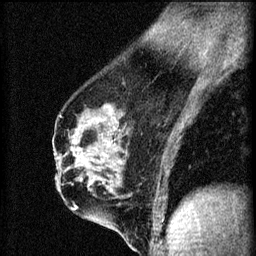
Breast MRI (dynamic contrast-enhanced), one sagittal slice; position 38 of 60 along the scan axis; 3 images stored at this slice position (order not interpretable as contrast timing); 1.5 T; TE 4.2 ms, TR 8.2 ms; 2 mm slice thickness; 256 × 256 image matrix, field of view 180 × 180 mm. Female patient, age 56 years.
Outlined on this slice (semi-automatically segmented with operator editing):
- analysis volume of interest (the breast-tissue region the enhancement analysis was run in; not a lesion): bounding box (x1, y1, x2, y2) in pixels: (62, 136, 111, 179)
- tumour enhancement mask (voxels above the 70 % enhancement threshold inside the analysis volume of interest): (76, 142, 110, 179)